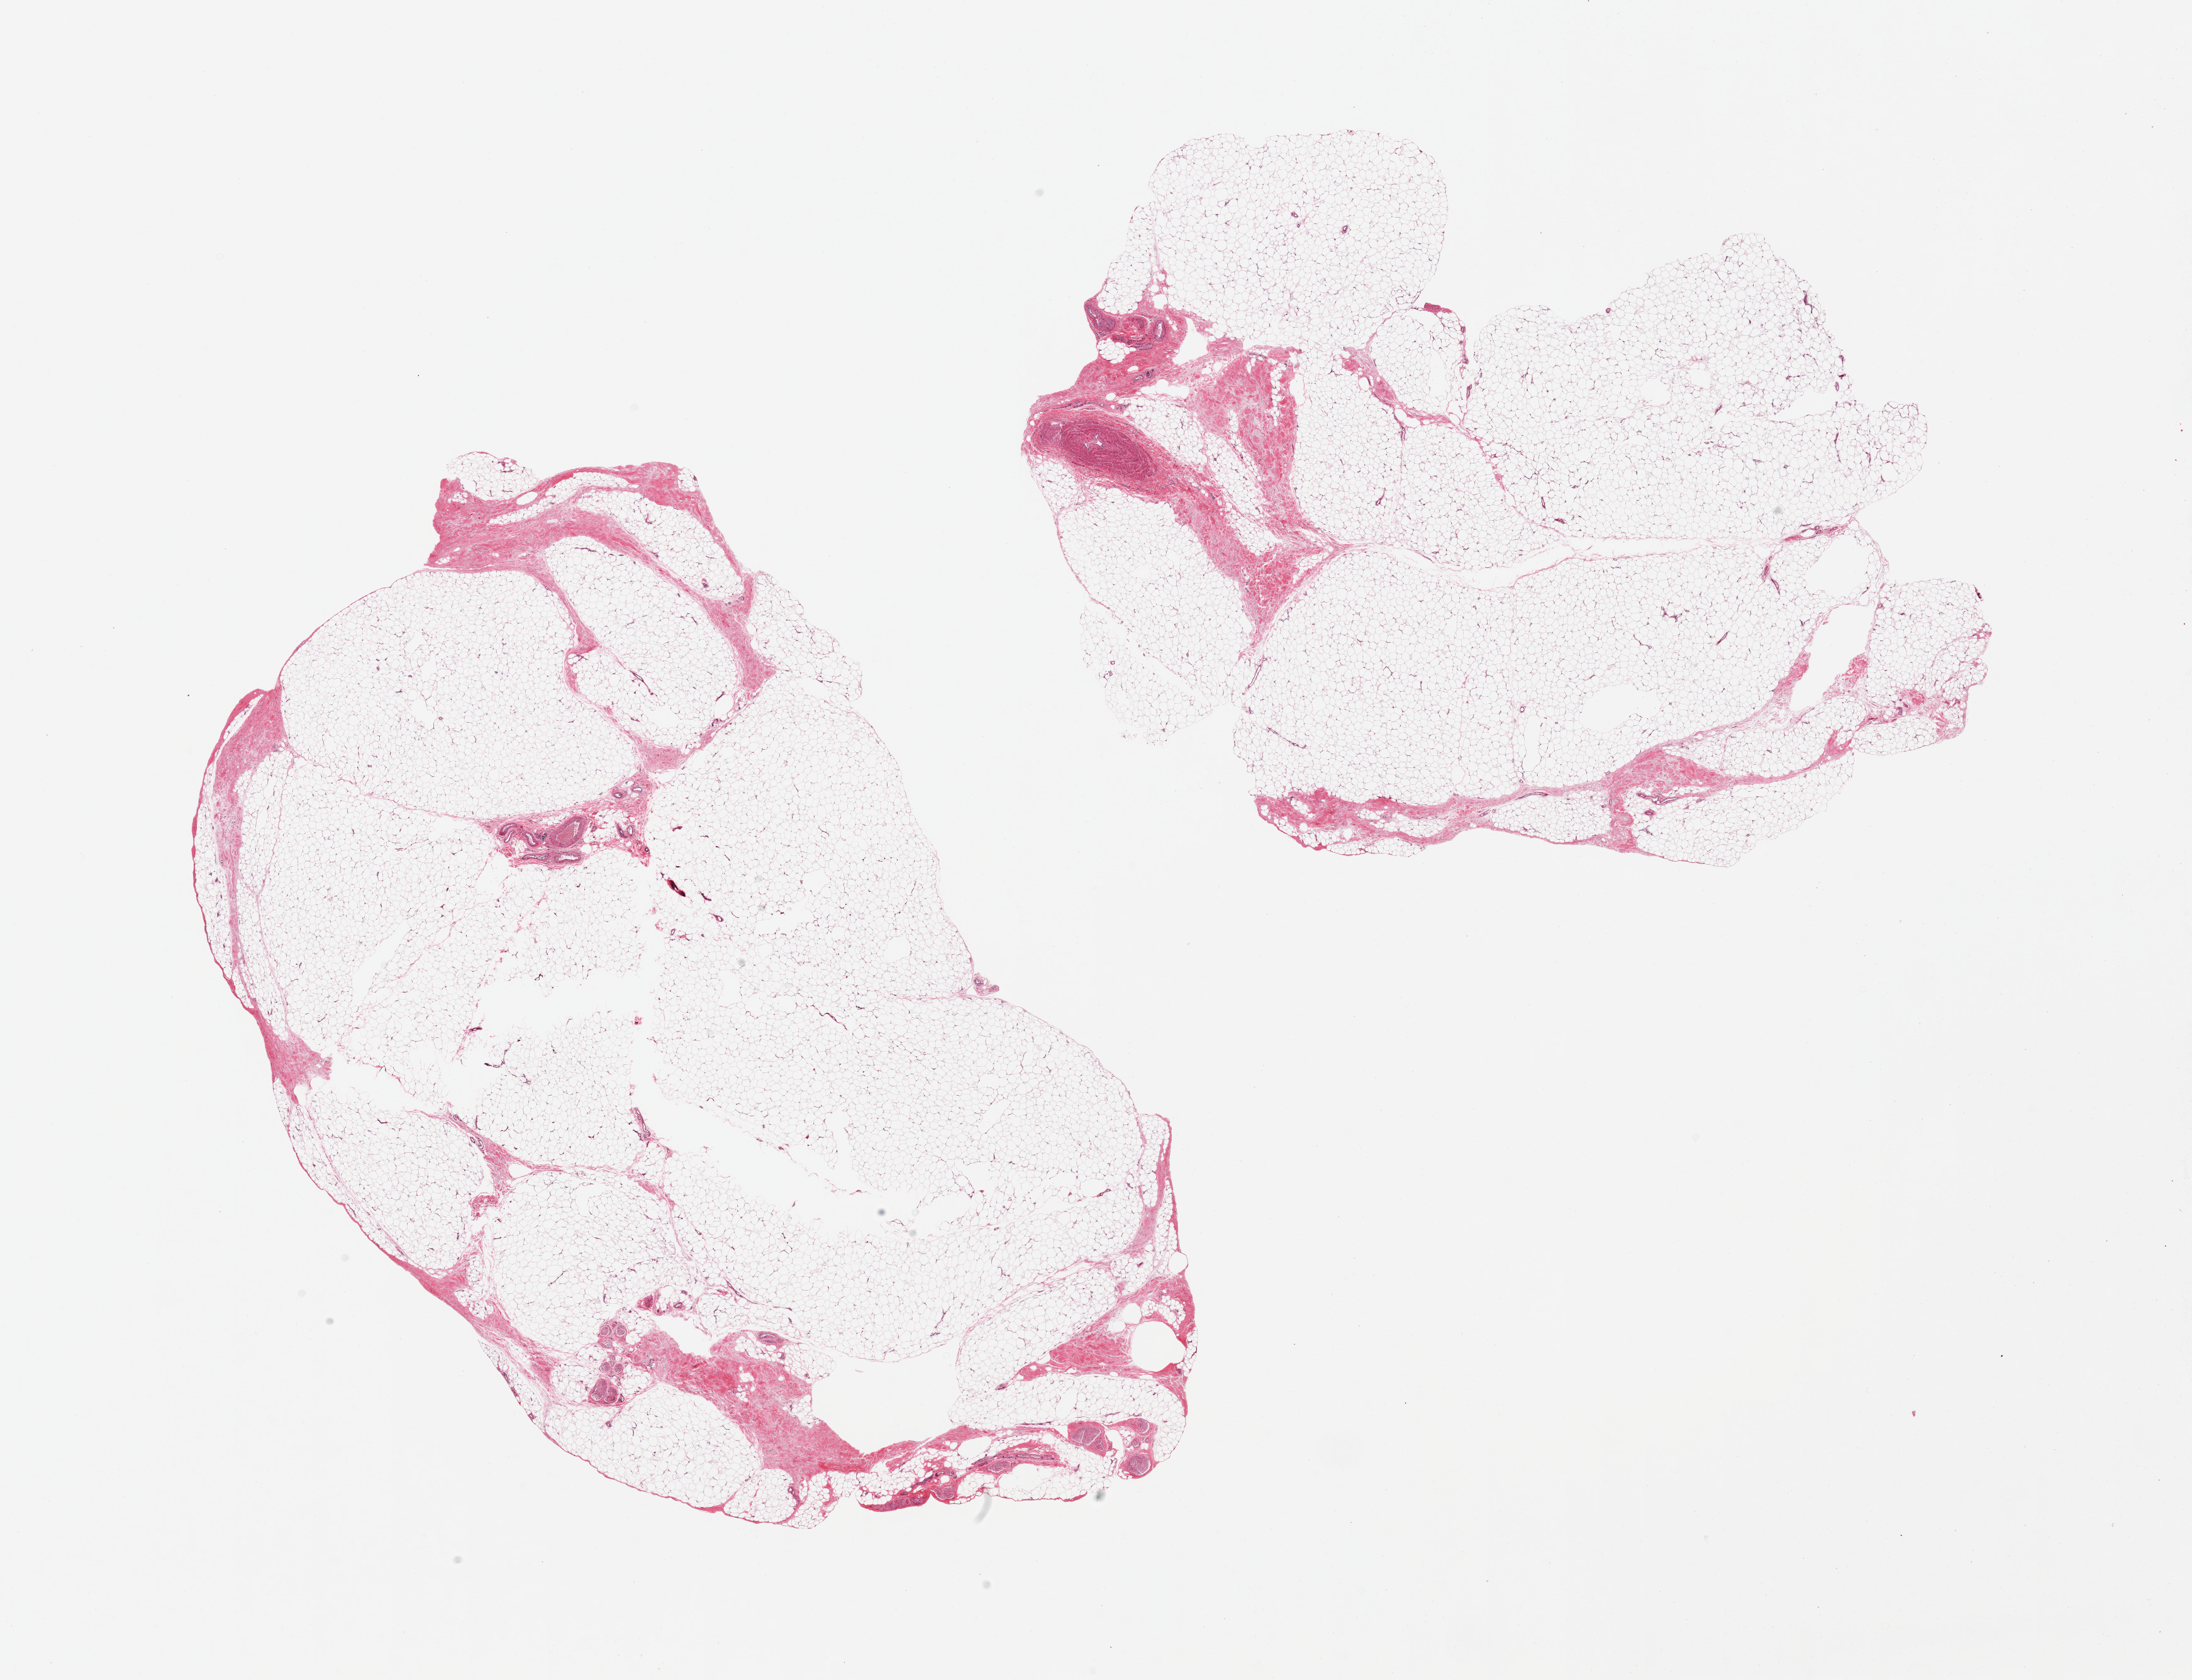
Whole-slide image, haematoxylin and eosin stain, brightfield — low-resolution overview of the scanned area, about 27.6 x 21.1 mm, PAXgene-fixed paraffin-embedded (PFPE) section, section of adipose tissue (target tissue), tissue donor sample.
Review note (as recorded): 2 pieces, both with ~10% fibrous tissue and nerve, few defects in one centrally (?poor fixation).